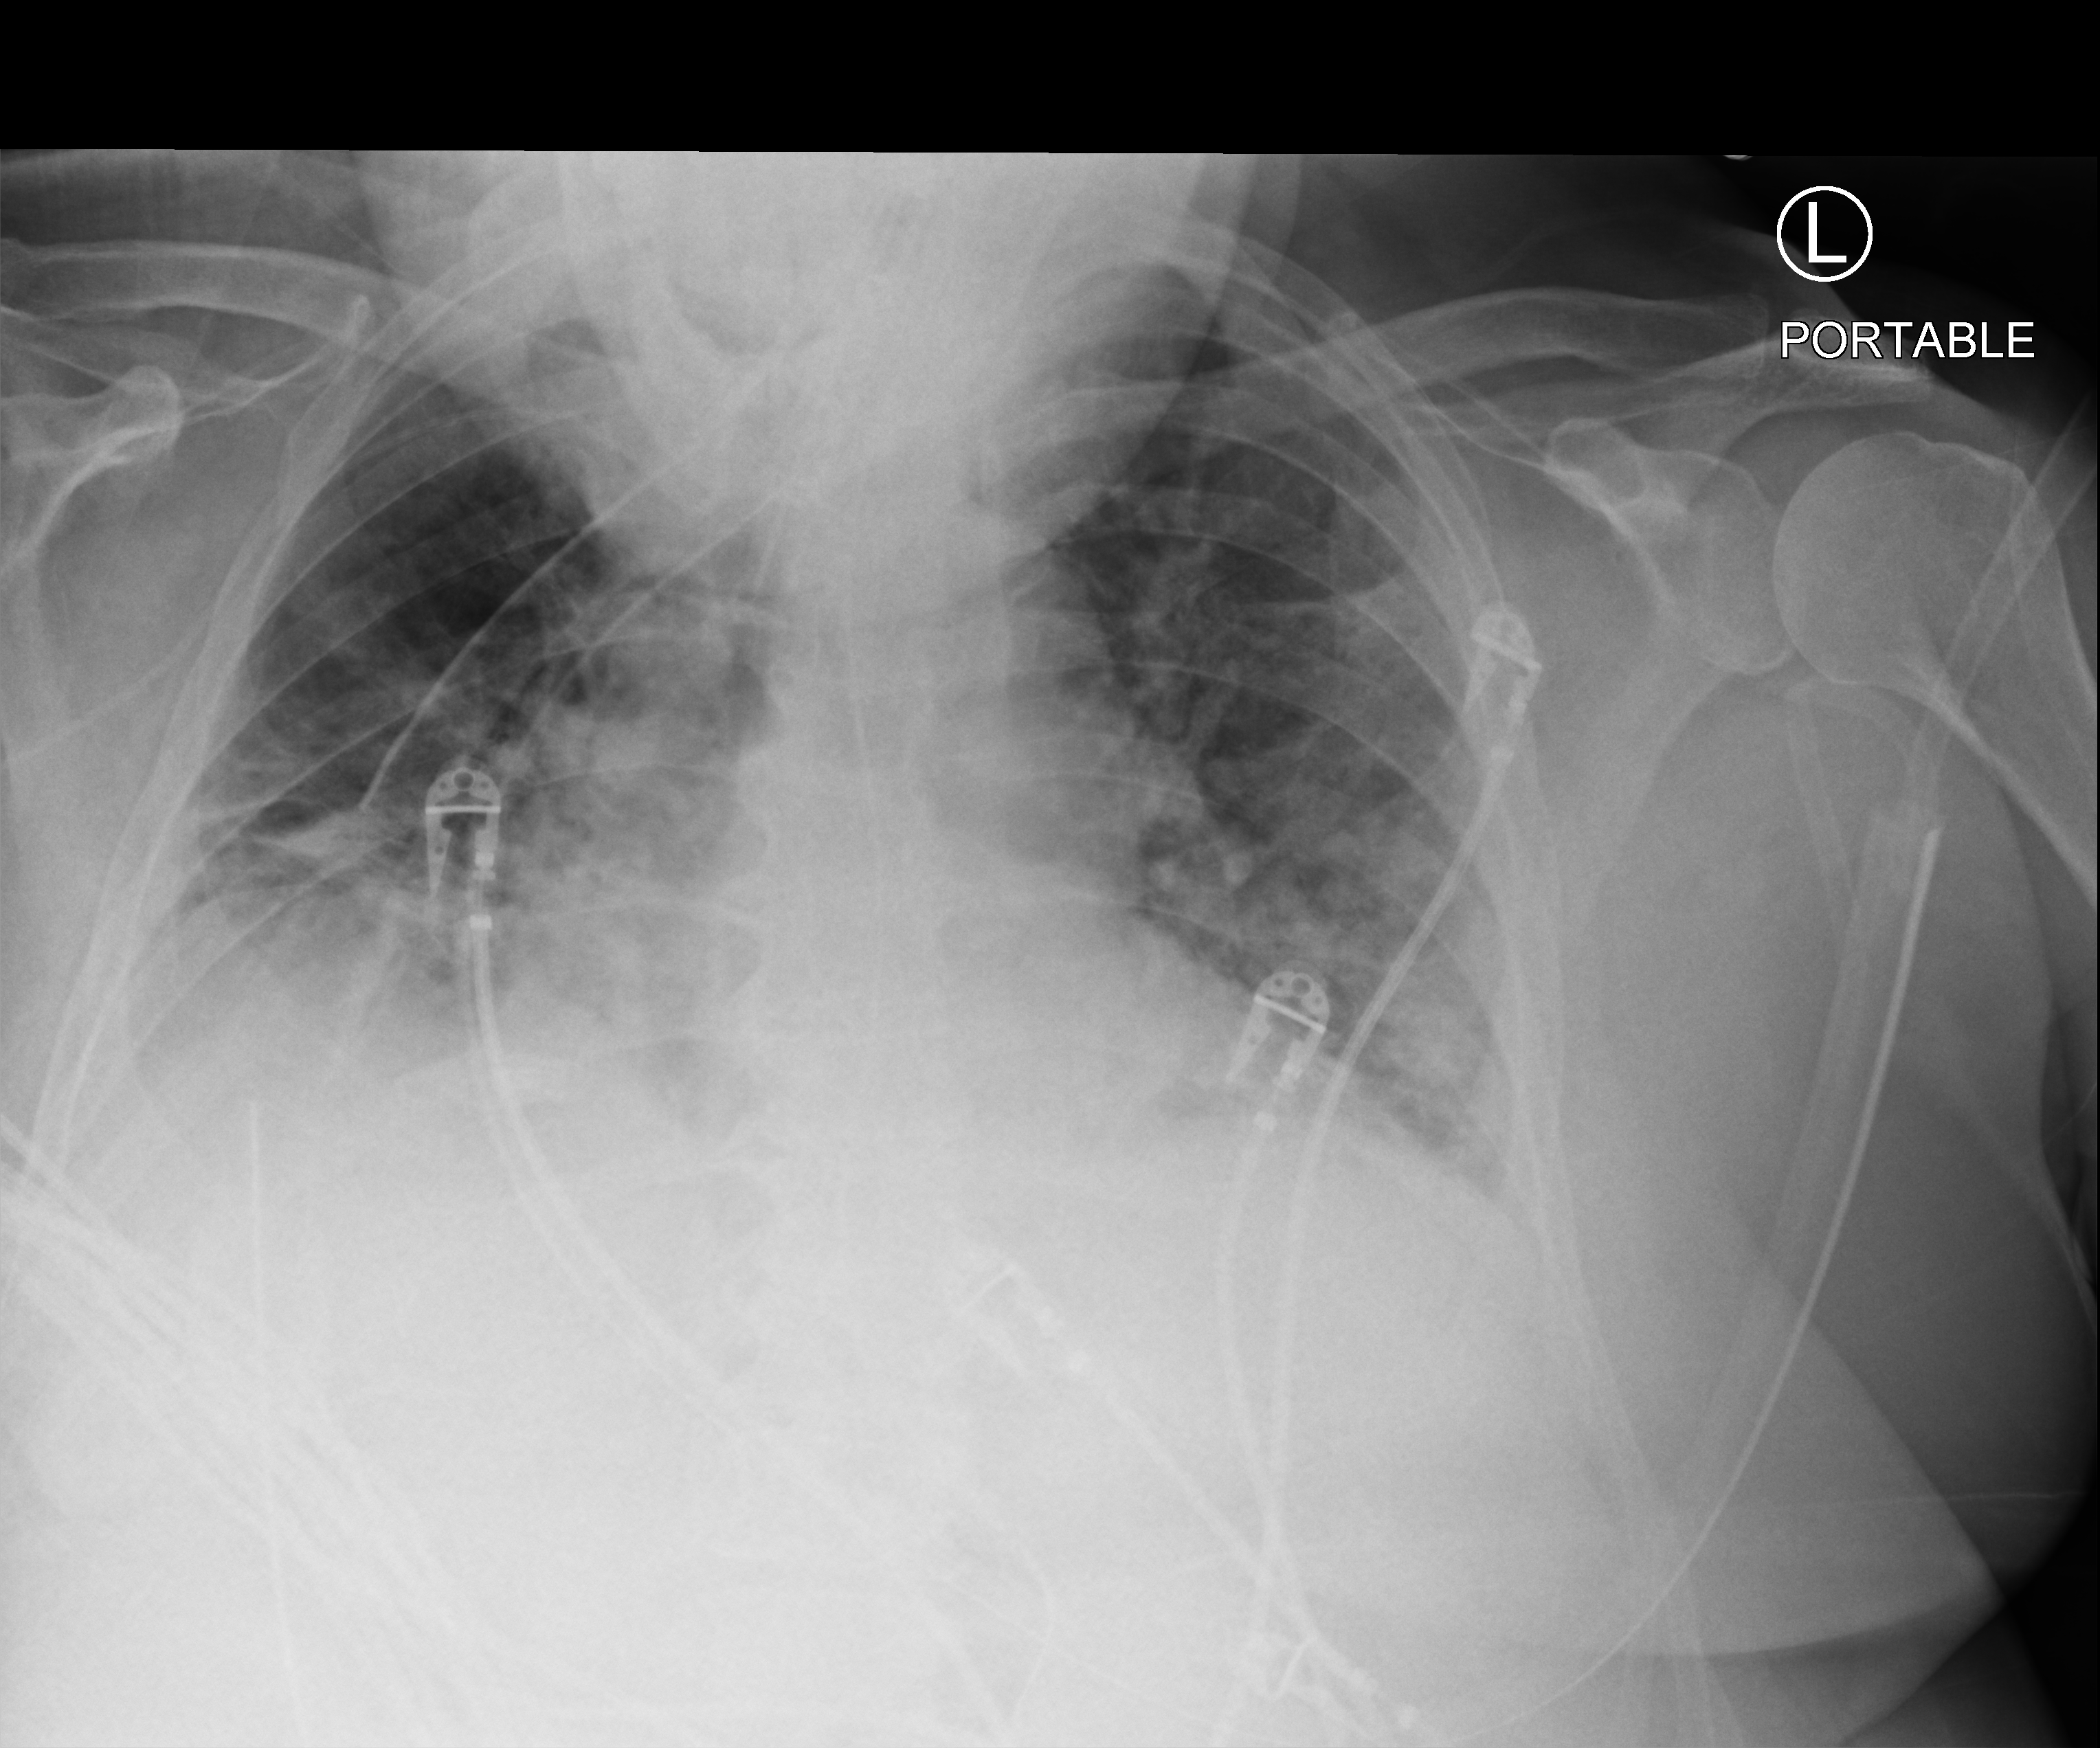
Portable chest radiograph, anteroposterior (AP) projection. Male patient hospitalised with COVID-19, age 60–74 years.
From the hospital-stay record, not from the radiograph (when in the stay this image was taken is not recorded):
- chronic kidney disease (admission record): no
- COPD (admission record): no
- length of hospital stay: 26 days